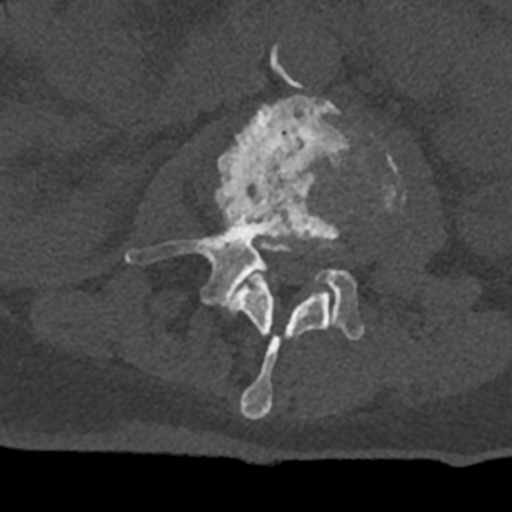
CT including the spine, one axial slice. Slice 346 of 797 in the series (ordered by position). Reconstruction kernel Br40s/3. 120 kVp. Bone window (W 1800 / L 400 HU). 0.5 mm slice thickness. 512 × 512 image matrix. Patient: male, 74 years. From the clinical record (not read from this slice): primary cancer: renal; vertebrae with lytic lesions (as recorded): T10, L1, L2, L3, L4, L5.
Outlined on this slice (semi-automatic segmentation, software-assisted and operator-edited):
- L2 vertebra: bounding box (x1, y1, x2, y2) in pixels: (228, 265, 331, 420)
- L3 vertebra: (125, 94, 404, 340)